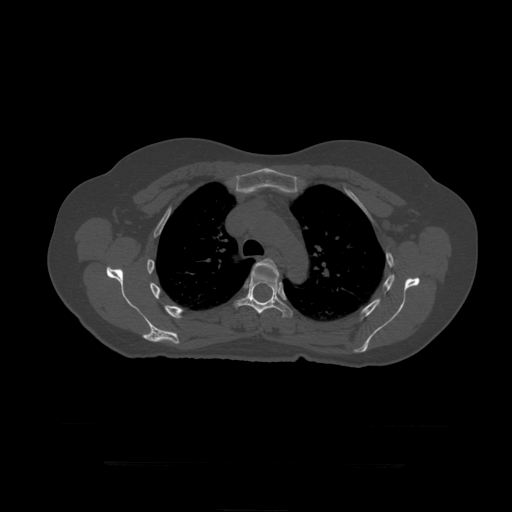
CT including the spine, one axial slice. Position 323 of 399 along the scan axis. 120 kVp. Bone window (W 1800 / L 400 HU). 512 × 512 image matrix, field of view 450 × 450 mm. Patient age 41 years. Case-level facts recorded for this patient, not image findings: primary cancer: breast.
Outlined on this slice (semi-automatic segmentation, software-assisted and operator-edited):
- T5 vertebra: bounding box [x1, y1, x2, y2] px = [253, 259, 280, 281]
- T6 vertebra: [234, 270, 293, 318]